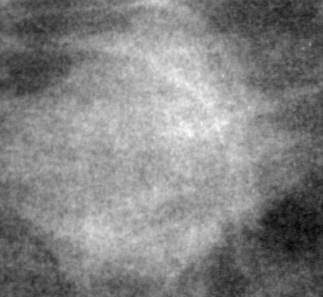
Region of interest cut from a scanned film mammogram (one marked finding), right breast, MLO view.
Finding: mass, shape lobulated, margins ill defined; BI-RADS assessment category 4; pathology result (as recorded, not read from the image): benign.